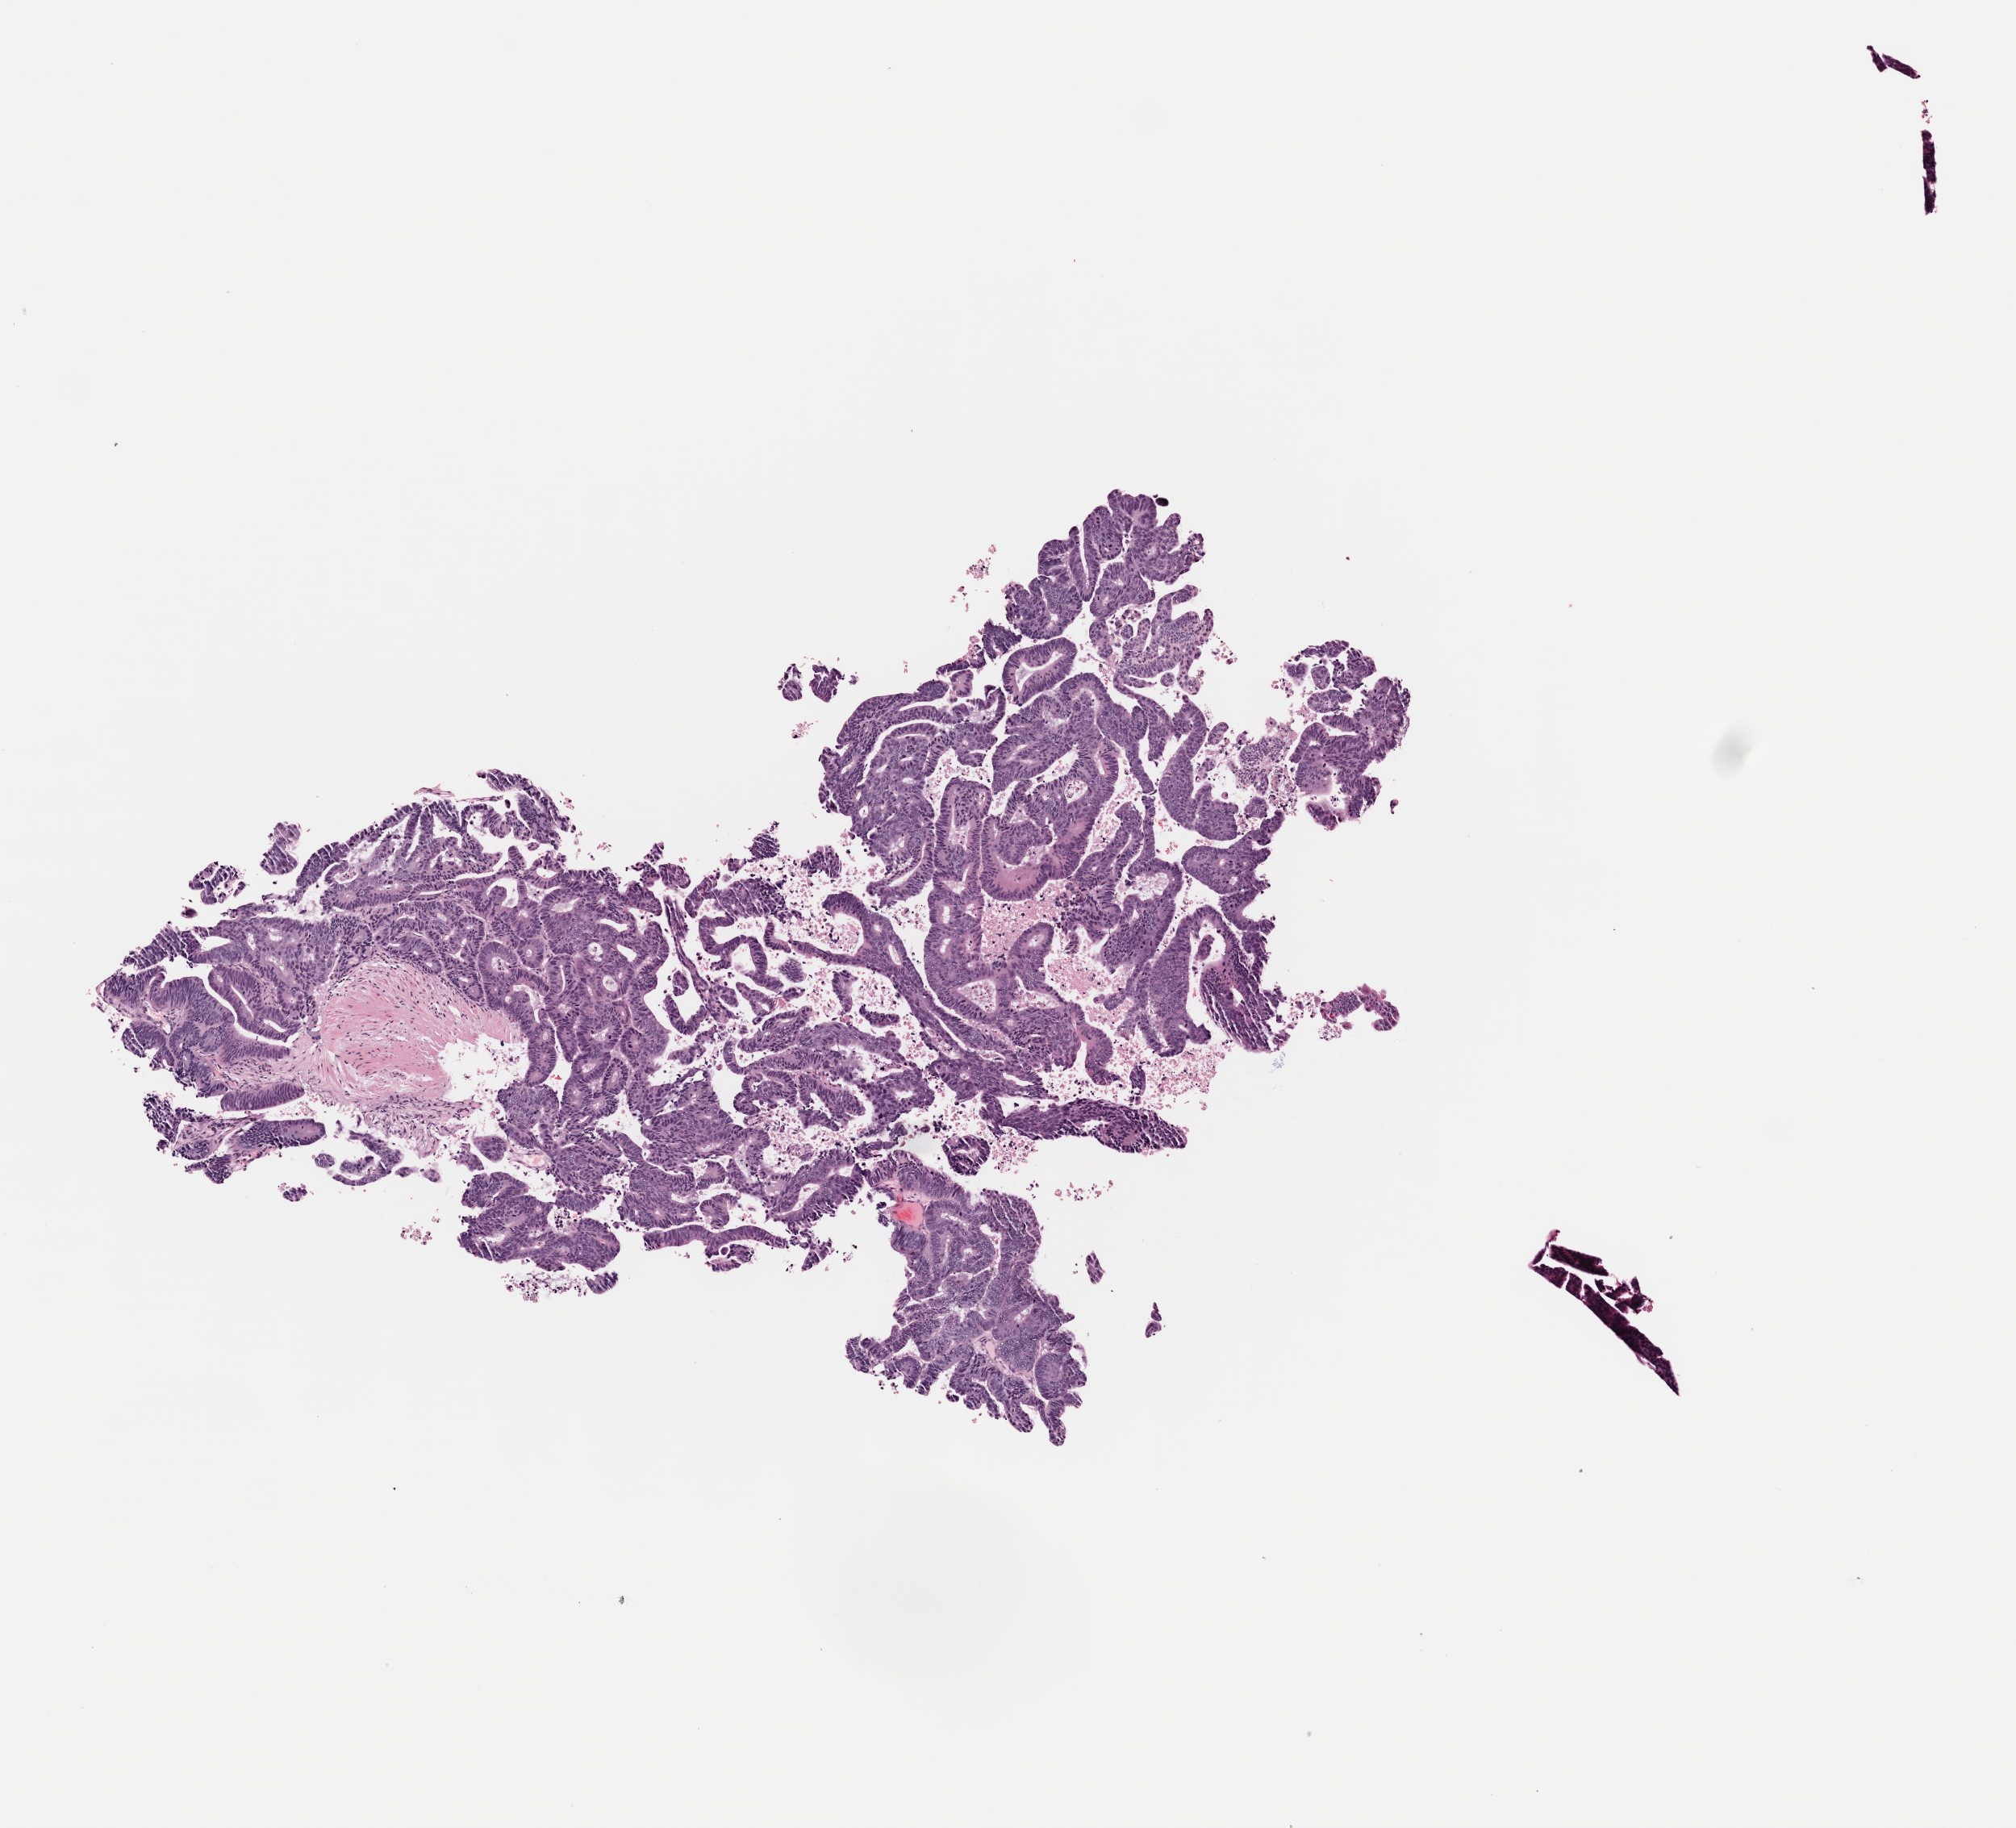
Whole-slide histology image, H&E, low-resolution overview of the scanned area, about 4.9 x 4.5 mm (from a 40x scan), frozen section, colon, primary tumour sample. Patient: male, age at initial diagnosis 82 years. Pathologist review of this section (percent, as recorded): tumour cells 70%, tumour nuclei 85%, normal cells 0%, stromal cells 20%, necrosis 10%. Infiltration values recorded for this section: lymphocyte infiltration 3%, monocyte infiltration 1%, neutrophil infiltration 2%.
Pathologic diagnosis: Adenocarcinoma, NOS (ascending colon). AJCC pathologic stage: I.